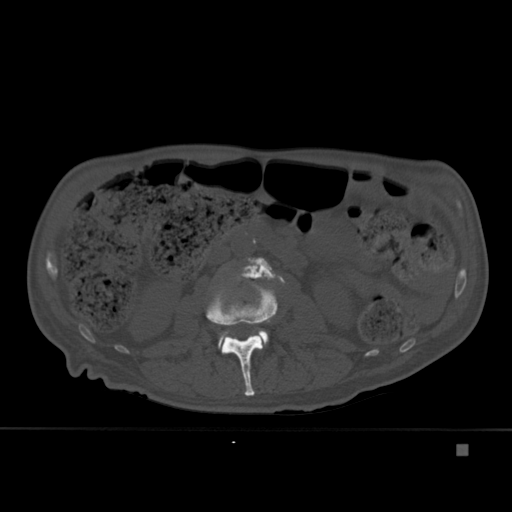
CT including the spine, one axial slice. Position 156 of 451 along the scan axis. Bone window (W 1800 / L 400 HU). 512 × 512 image matrix, field of view 378 × 378 mm. Patient: male, 75 years. From the clinical record (not read from this slice): primary cancer: prostate.
Outlined on this slice (semi-automatically segmented with operator editing):
- L2 vertebra: box from (x=206, y=276) to (x=278, y=396) px
- L3 vertebra: (x=221, y=257)–(x=285, y=350)